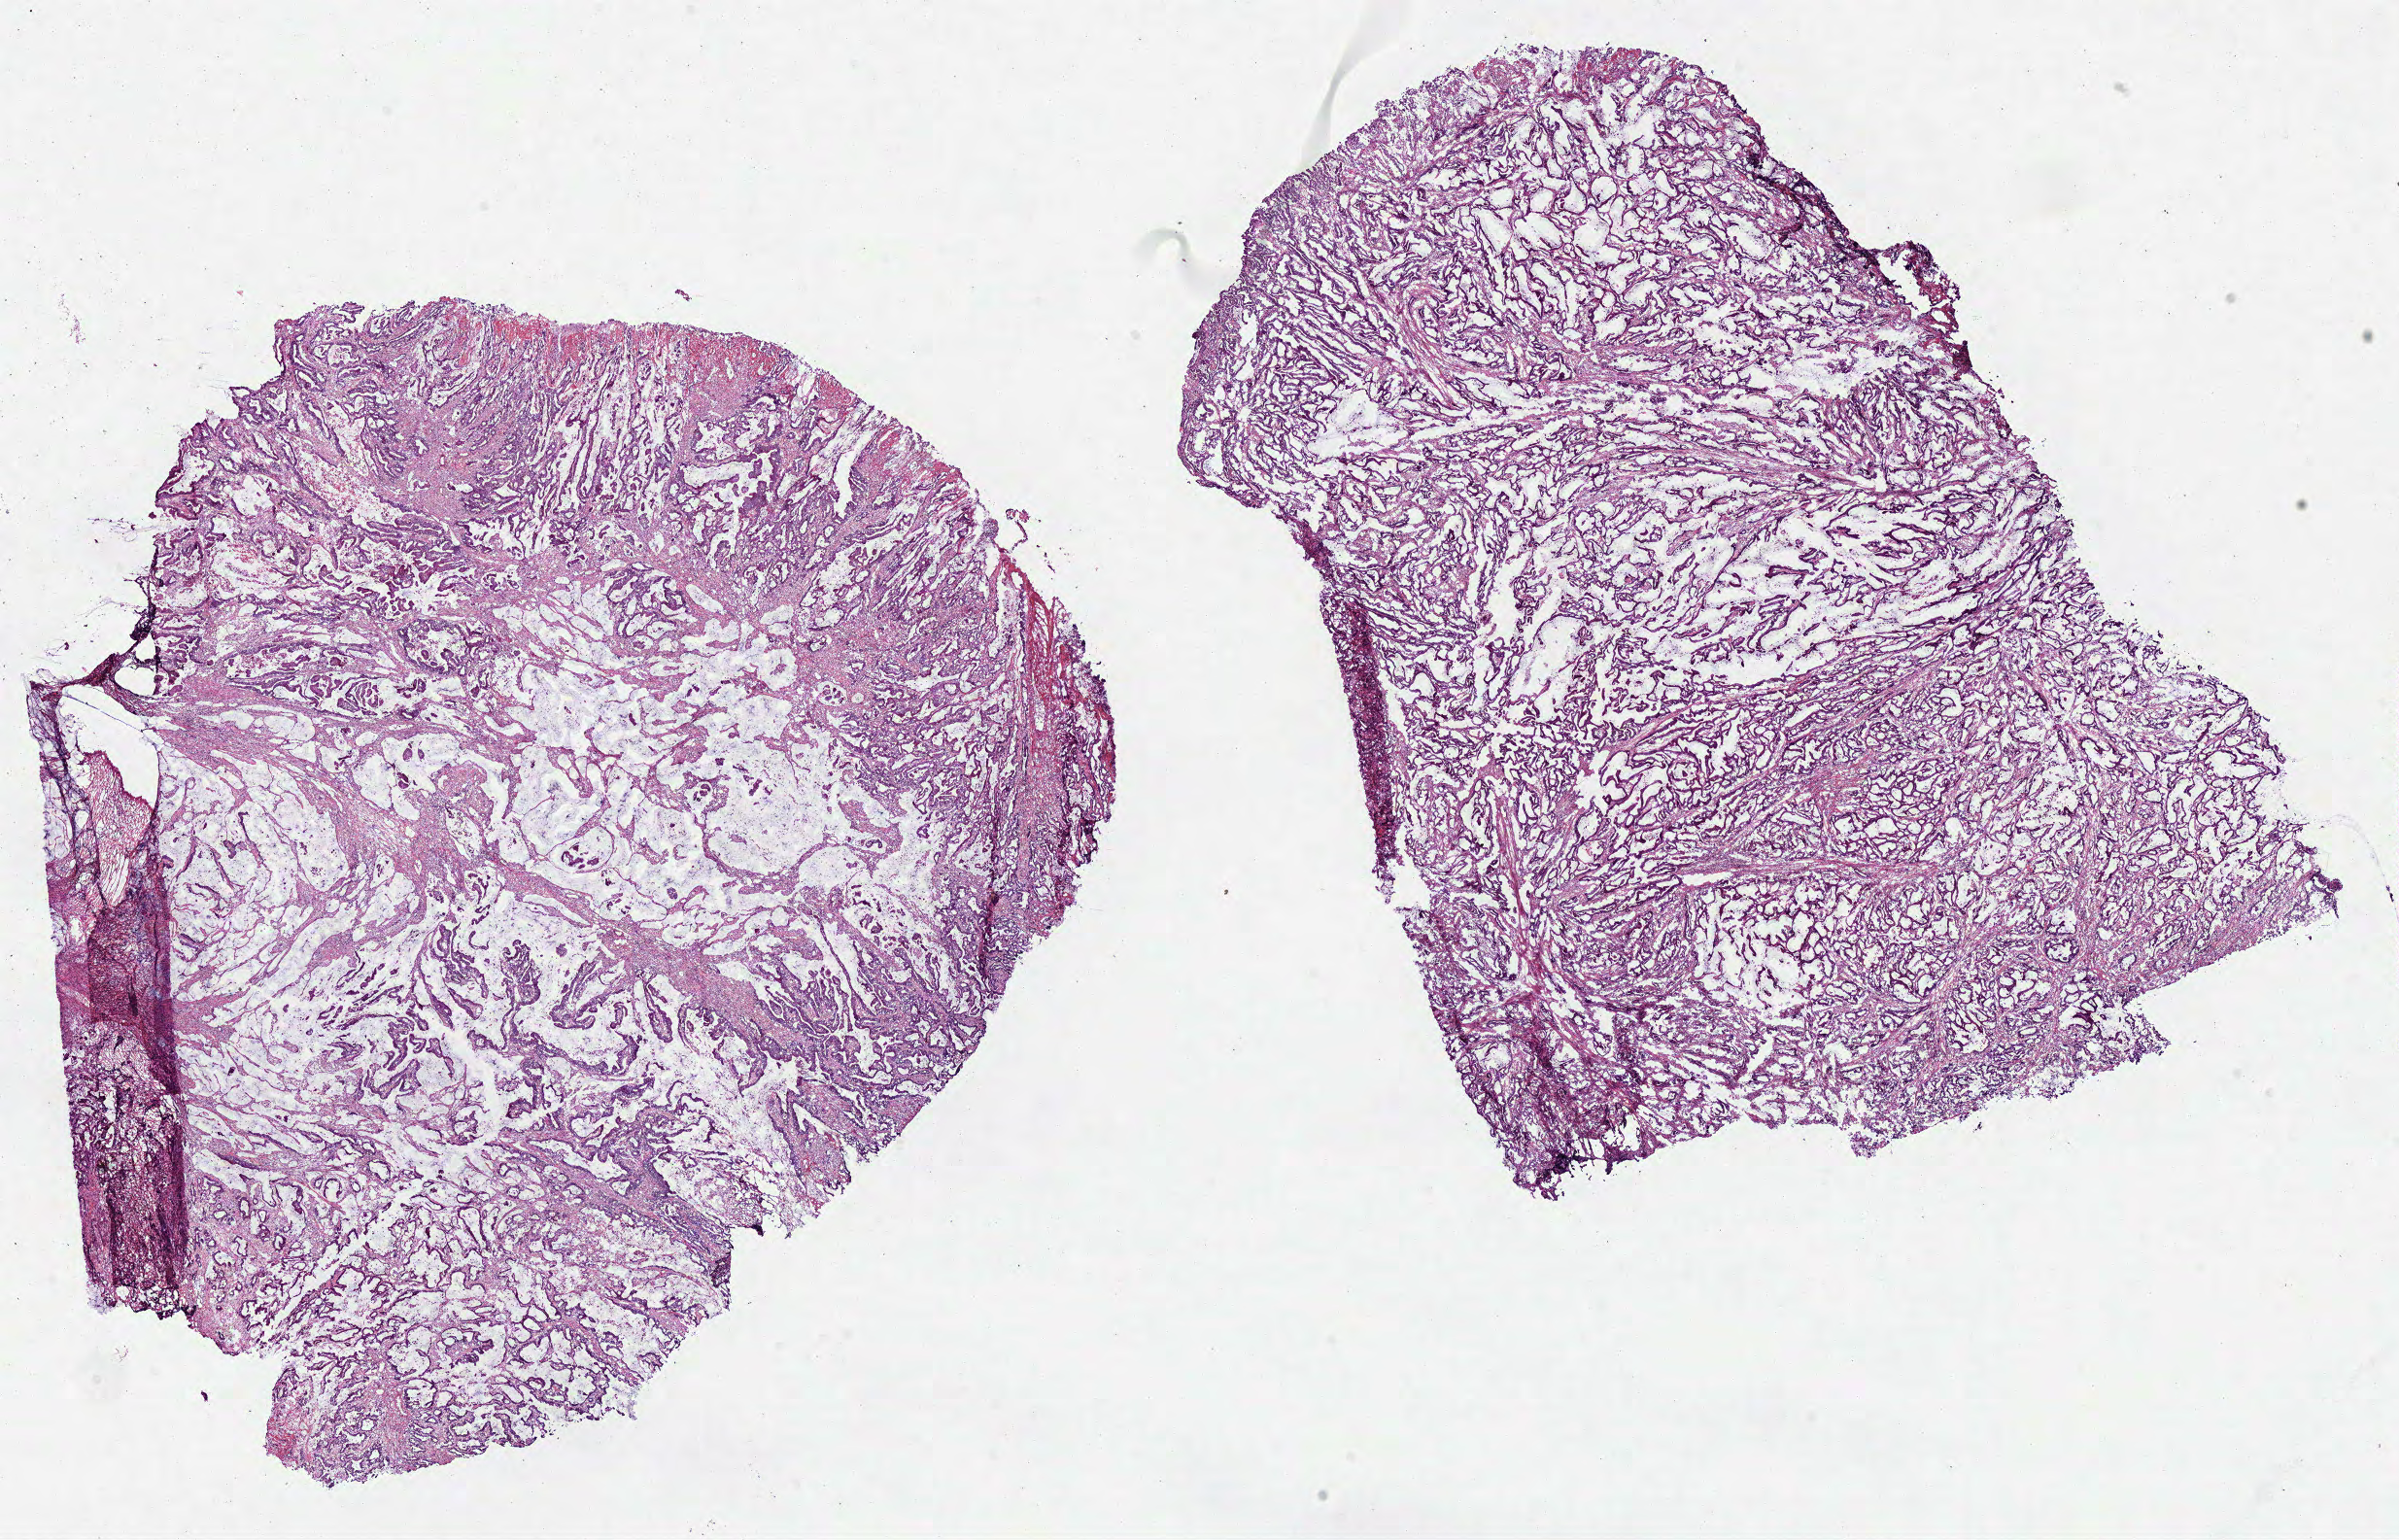
Digitized Hematoxylin and eosin (H&E) stained tissue section (whole slide), whole scanned area (about 19.5 x 12.5 mm) shown as a low-resolution overview; frozen section from the bottom of the tissue portion; colon, primary tumour sample. Female patient; age at initial diagnosis 58 years. Composition of this section per pathologist review: tumour cells 85%, tumour nuclei 85%, normal cells 0%, stromal cells 15%, necrosis 0%.
AJCC pathologic stage: IIA. Histologic diagnosis: Adenocarcinoma, NOS (cecum). Lymph nodes positive (case pathology): 0 of 15 examined.